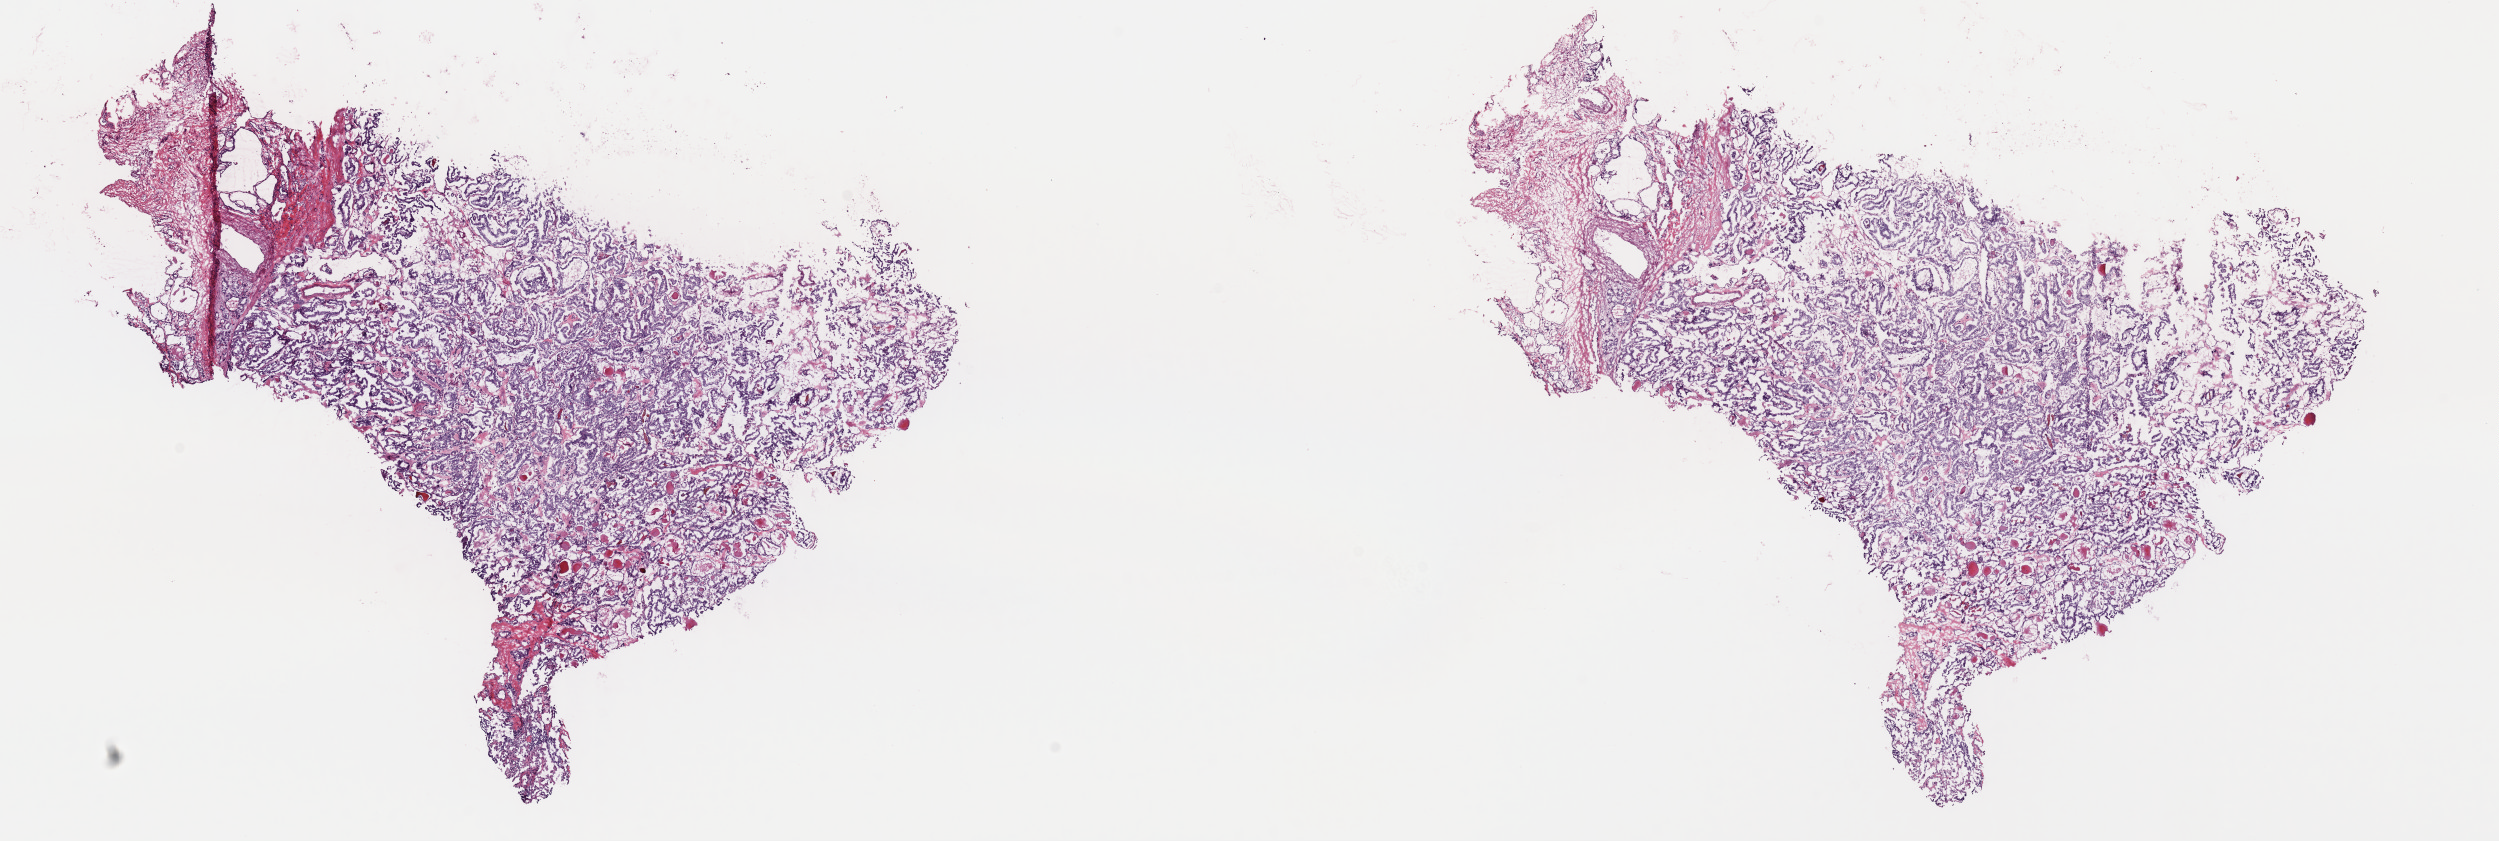
Digitized H&E-stained tissue section (whole slide), a low-resolution overview of the entire scanned area, about 19.7 x 6.6 mm, frozen section, sample: primary tumour, thyroid. Patient: male, age at initial diagnosis 39 years. Slide review estimates, as recorded: tumour cells 88%, tumour nuclei 90%, normal cells 6%, stromal cells 6%, necrosis 0%. Inflammatory infiltration, as recorded: lymphocyte infiltration 0%, monocyte infiltration 0%, neutrophil infiltration 0%.
AJCC pathologic stage: I. Diagnosis: Papillary adenocarcinoma, NOS (thyroid gland).